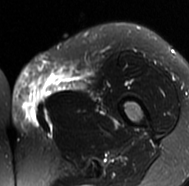
MRI of an extremity soft-tissue mass, one axial slice. Slice 25 of 77 in the series (ordered by position). T2-weighted fat-saturated. MR volume resampled by the dataset authors to the PET/CT grid (not the native acquisition matrix). 3.27 mm slice thickness. 189 × 186 image matrix, field of view 185 × 182 mm. Female patient. From the clinical record (not read from this slice): histological type: leiomyosarcoma; grade: high; site of the primary tumour: groin.
Annotated regions visible in this slice (expert contour drawn on MRI and transferred to this co-registered scan by the dataset authors):
- gross tumour volume including surrounding oedema: box from (x=10, y=56) to (x=96, y=131) px